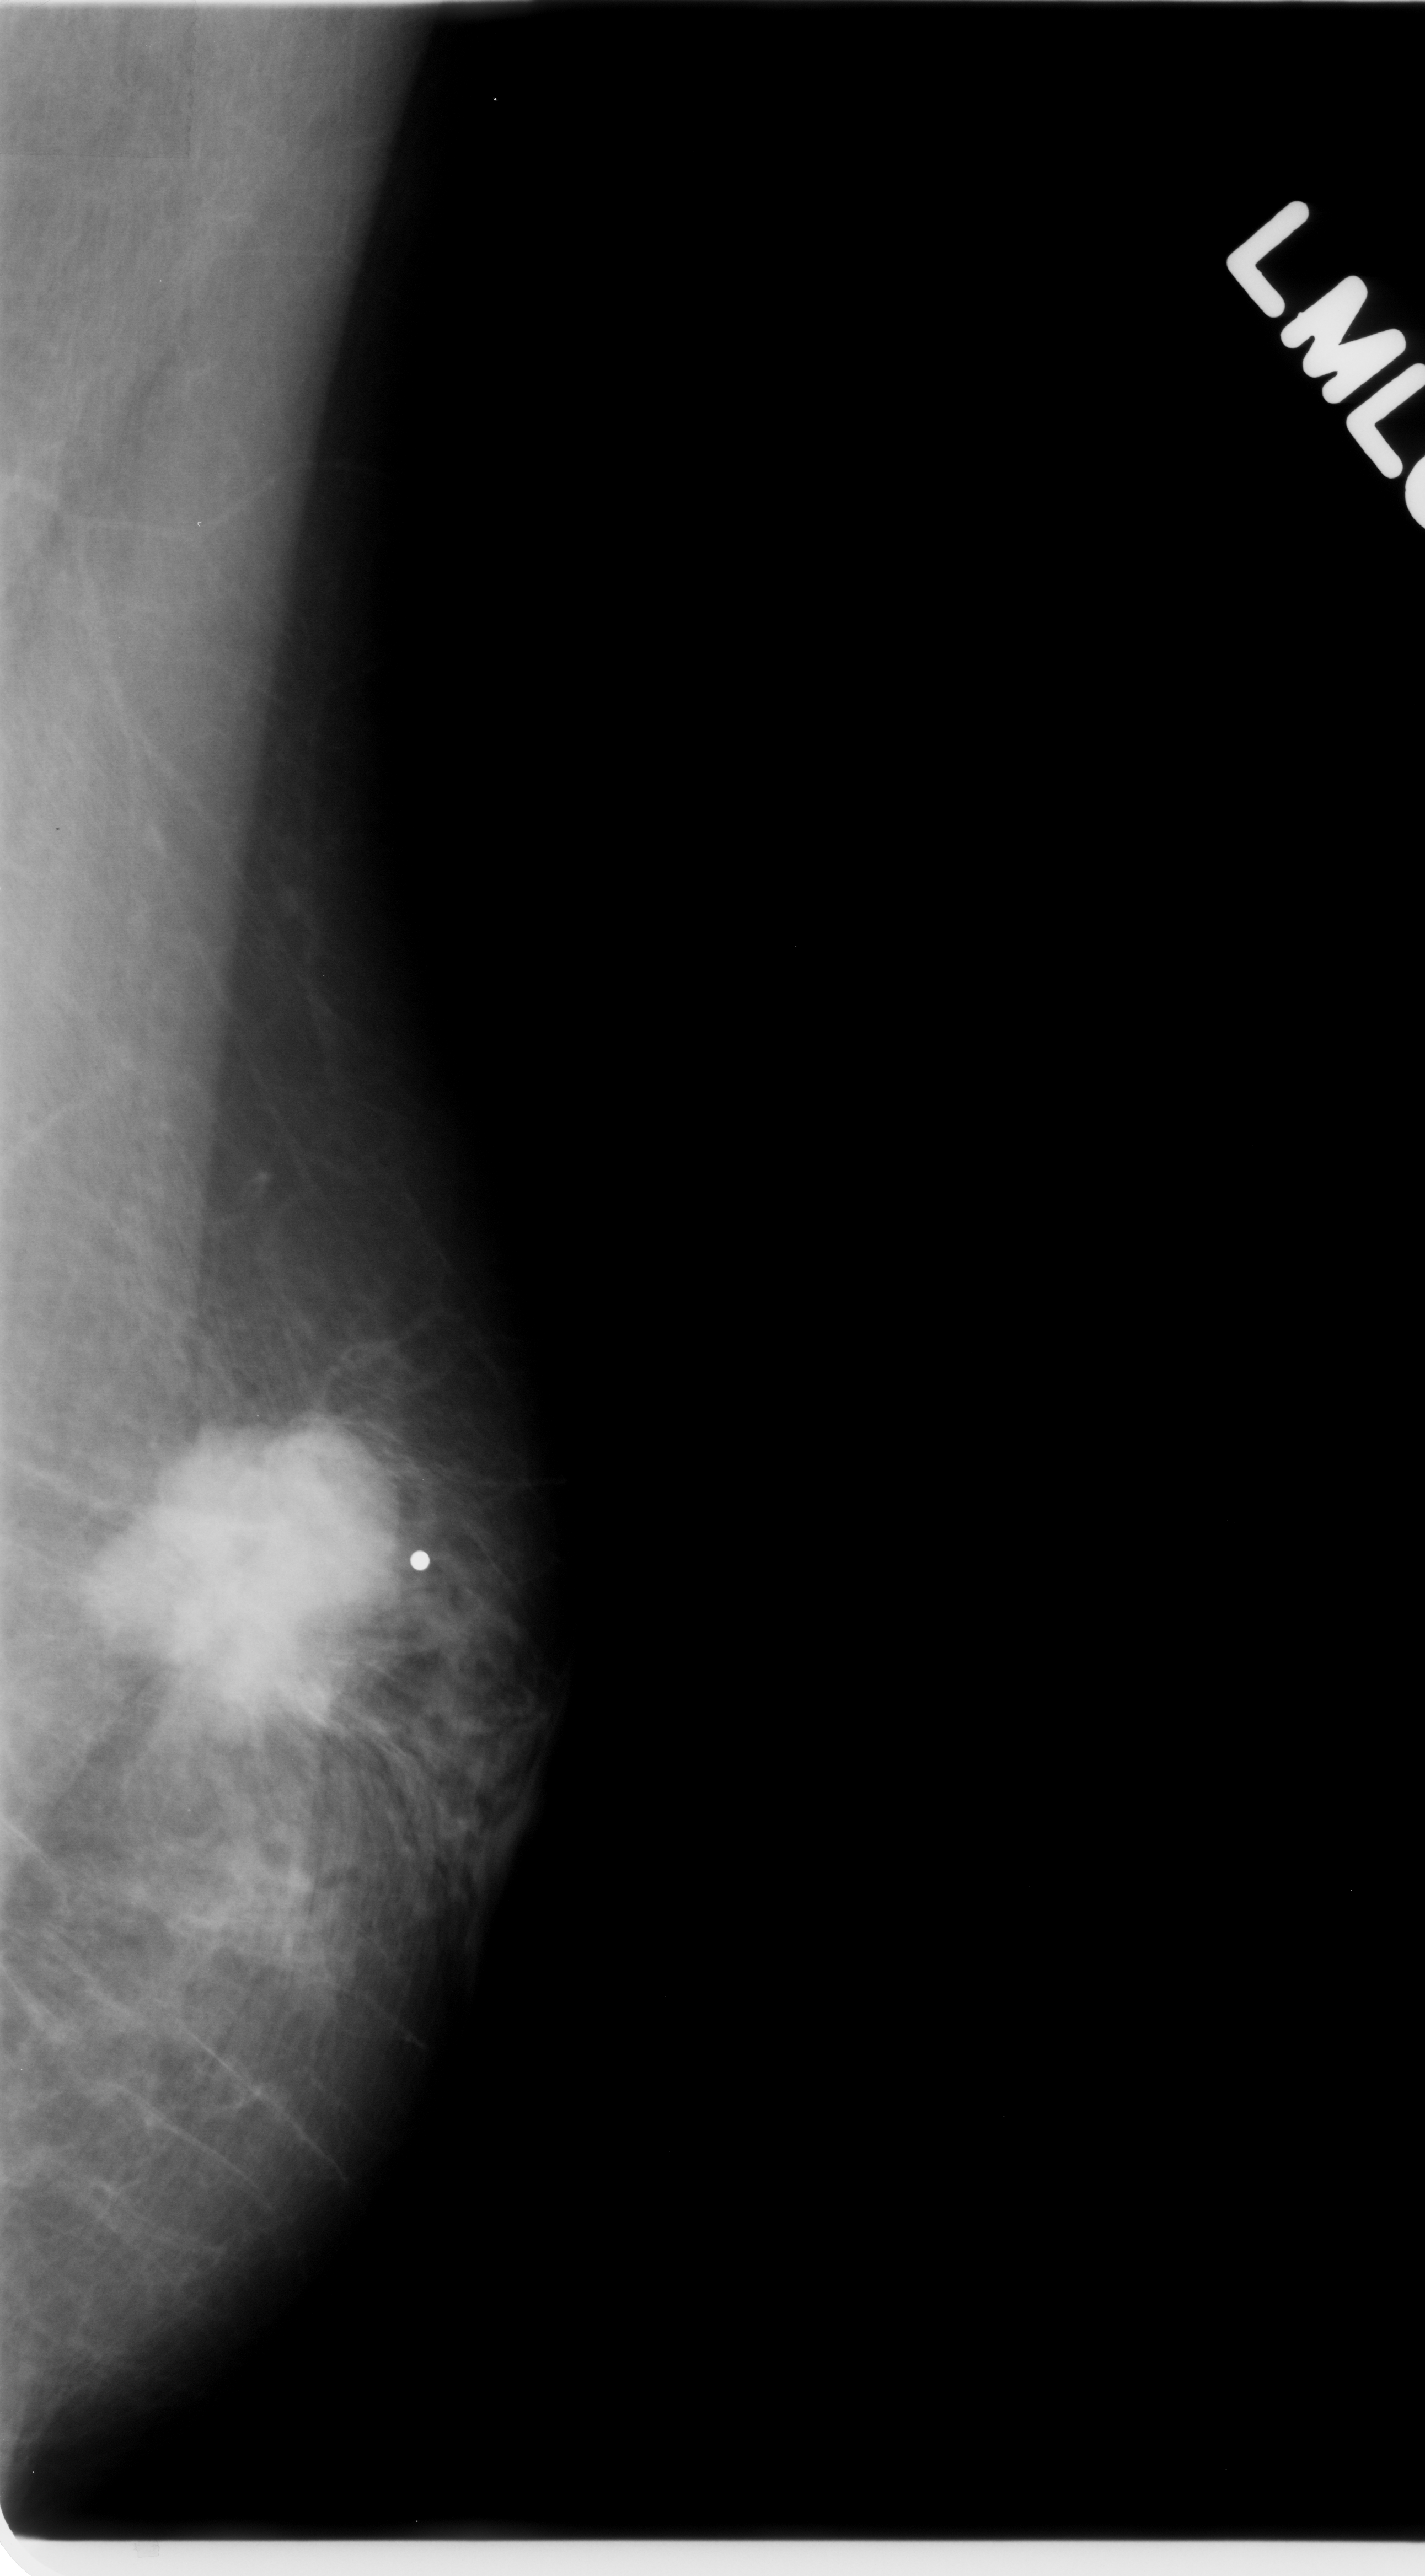
Digitized screen-film mammogram. Left breast. Mediolateral oblique (MLO) view. BI-RADS breast density category 2 (scale 1–4). 1425 × 2576 image matrix.
Expert-marked regions of interest on this film, with their recorded descriptors:
- mass, shape irregular, margins spiculated; BI-RADS assessment category 5; subtlety rating 5 on a 1 (subtle) to 5 (obvious) scale; pathology result (as recorded, not read from the image): malignant: bounding box <126,1386,401,1752> (left, top, right, bottom; pixels)